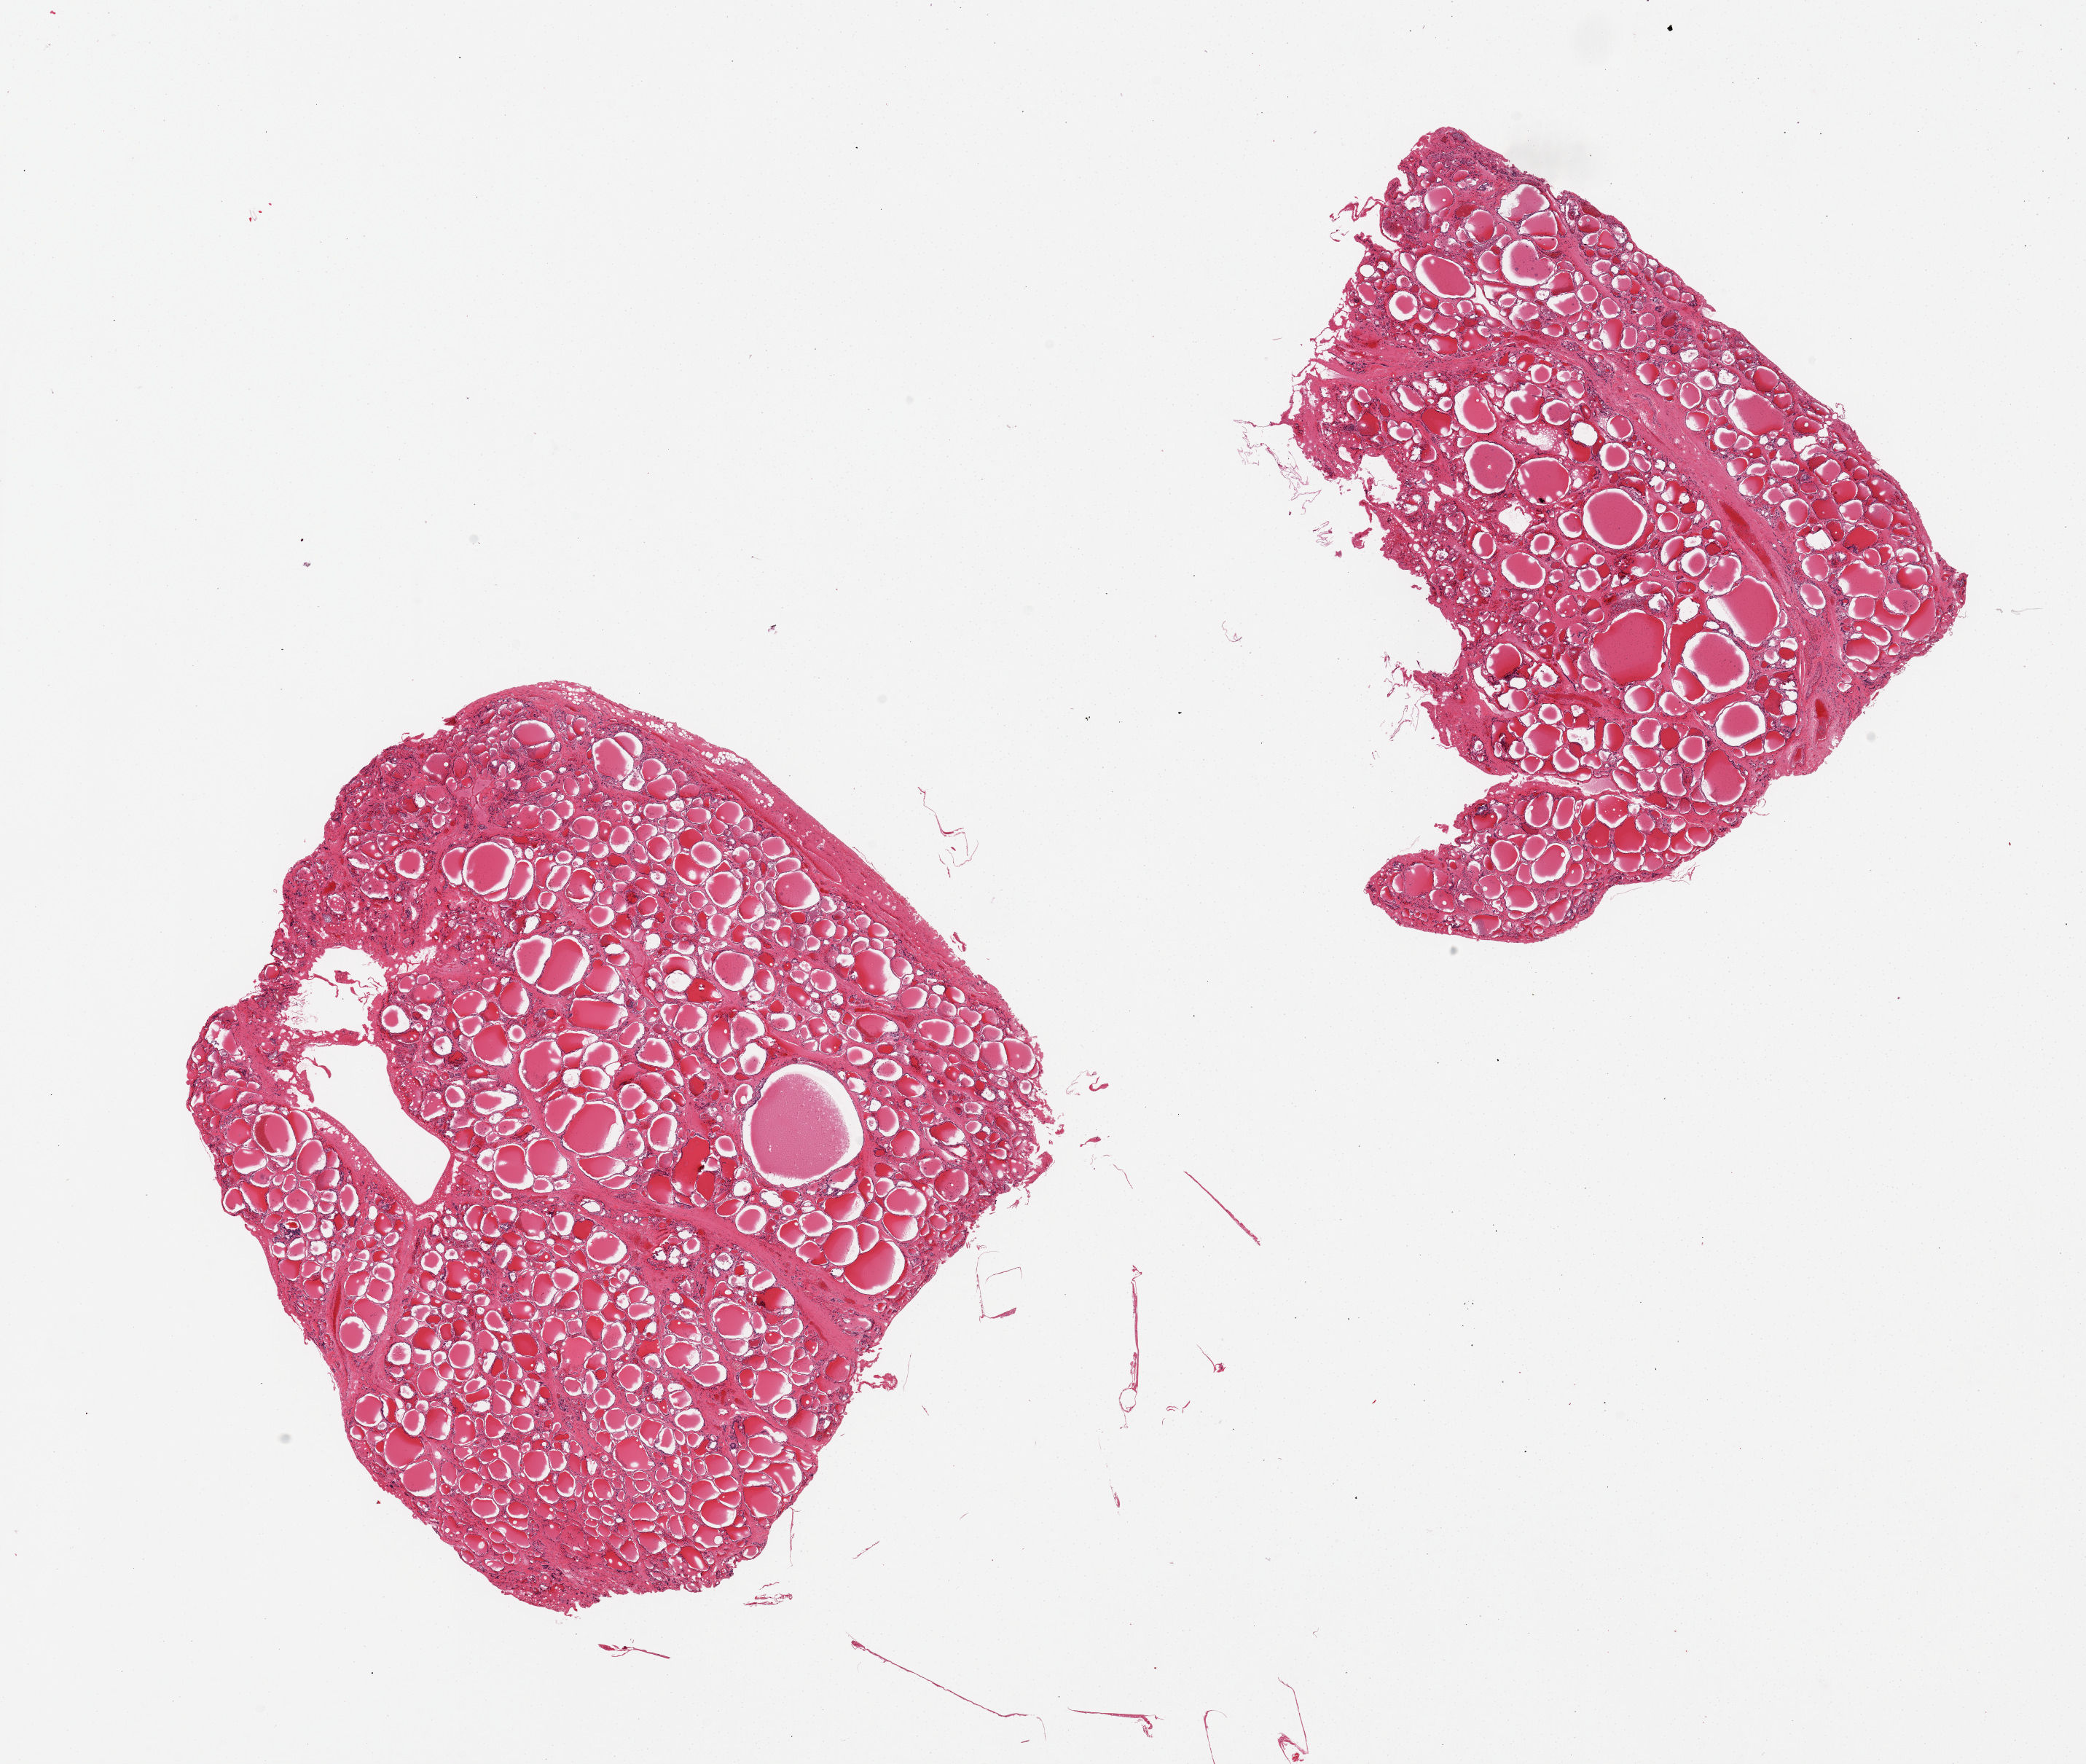
Digitized H&E-stained section, brightfield, low-resolution overview of the scanned area, about 22.6 x 19.1 mm (acquisition: 20x scan); PAXgene-fixed paraffin-embedded (PFPE) section; section of thyroid (target tissue); tissue donor sample. Donor sex: female.
Pathologist's review note for this sample: 2 pieces, incidental 1mm cyst.